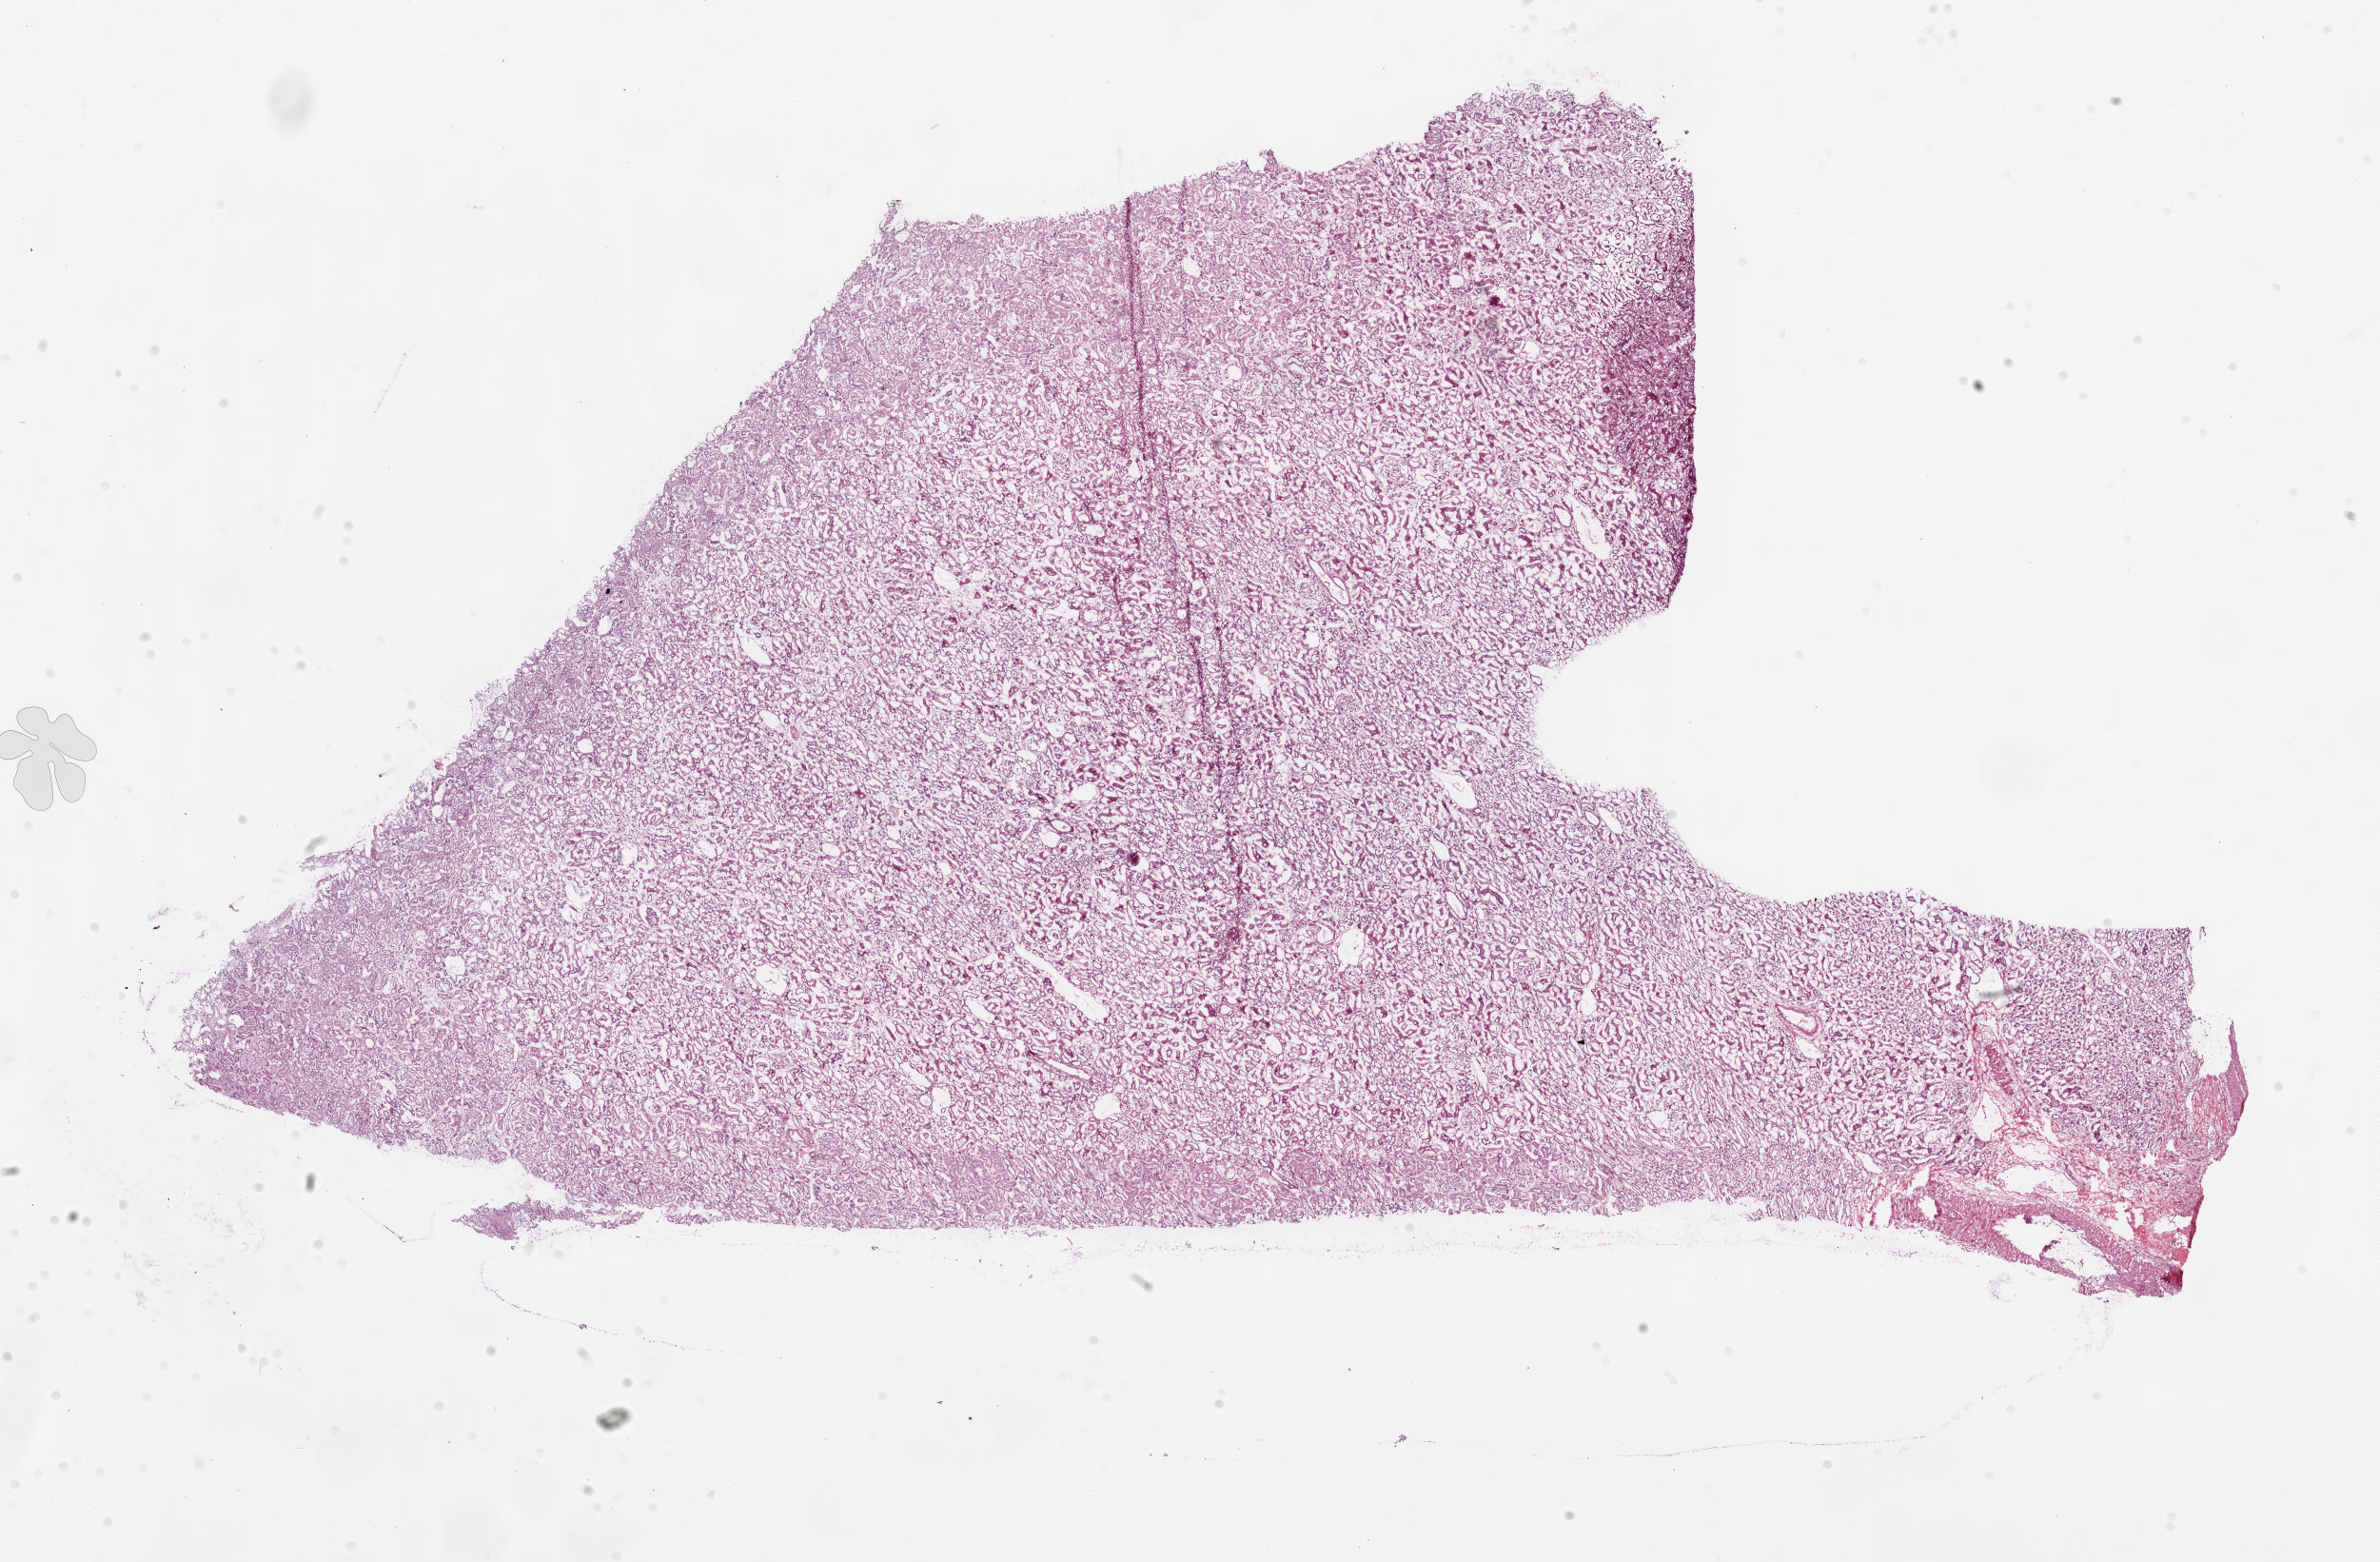
Digitized H&E-stained tissue section (whole slide) — low-resolution overview of the scanned area, about 19.8 x 13.0 mm (slide scanned at 20x), frozen section, kidney, solid tissue normal (non-tumour tissue) sample. Female, age 66 years at initial diagnosis.
• this section: solid tissue normal sample (biorepository sample class)
• patient diagnosis: Clear cell adenocarcinoma, NOS